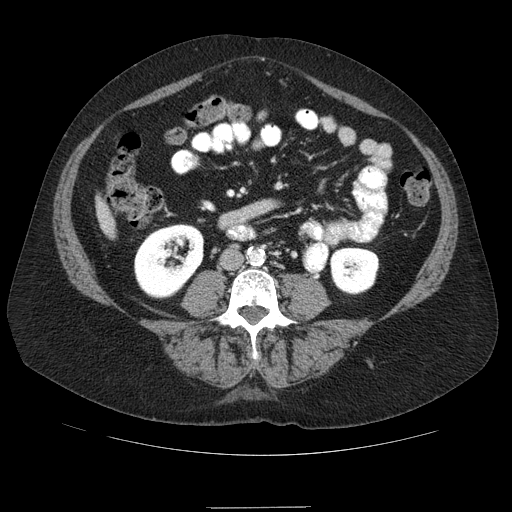
Contrast-enhanced abdominal CT (liver protocol), one axial slice; position 10 of 89 along the scan axis; soft-tissue window (W 400 / L 40 HU); 2.5 mm slice thickness; 512 × 512 image matrix, field of view 400 × 400 mm. From the clinical record (not read from this slice): diagnosis: hepatocellular carcinoma (patient treated with transarterial chemoembolisation; whether this scan precedes or follows treatment is not stated here); TNM stage (as recorded): Stage-IIIB; Child-Pugh class: A.
Outlined on this slice (semi-automatically segmented with operator editing):
- liver parenchyma outside the tumour (the mass and vessels are separate outlines, so this box may not span the whole liver): bounding box (x1, y1, x2, y2) in pixels: (96, 198, 114, 237)